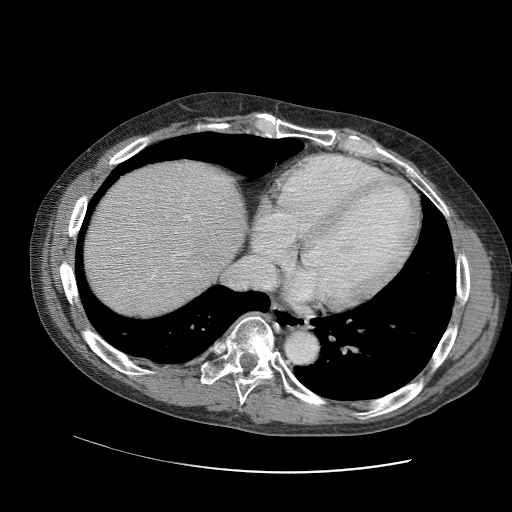
Contrast-enhanced abdominal CT (liver protocol), one axial slice; slice 90 of 109 in the series (ordered by position); reconstruction kernel STANDARD; 120 kVp; soft-tissue window (W 400 / L 40 HU); 2.5 mm slice thickness; 512 × 512 image matrix, field of view 400 × 400 mm. From the clinical record (not read from this slice): diagnosis: hepatocellular carcinoma (patient treated with transarterial chemoembolisation; whether this scan precedes or follows treatment is not stated here); TNM stage (as recorded): Stage-IIIC; Child-Pugh class: B.
Structures marked on this image (semi-automatically segmented with operator editing):
- liver parenchyma outside the tumour (the mass and vessels are separate outlines, so this box may not span the whole liver): box from (x=82, y=158) to (x=246, y=318) px
- liver vessels: (x=124, y=187)–(x=222, y=277)